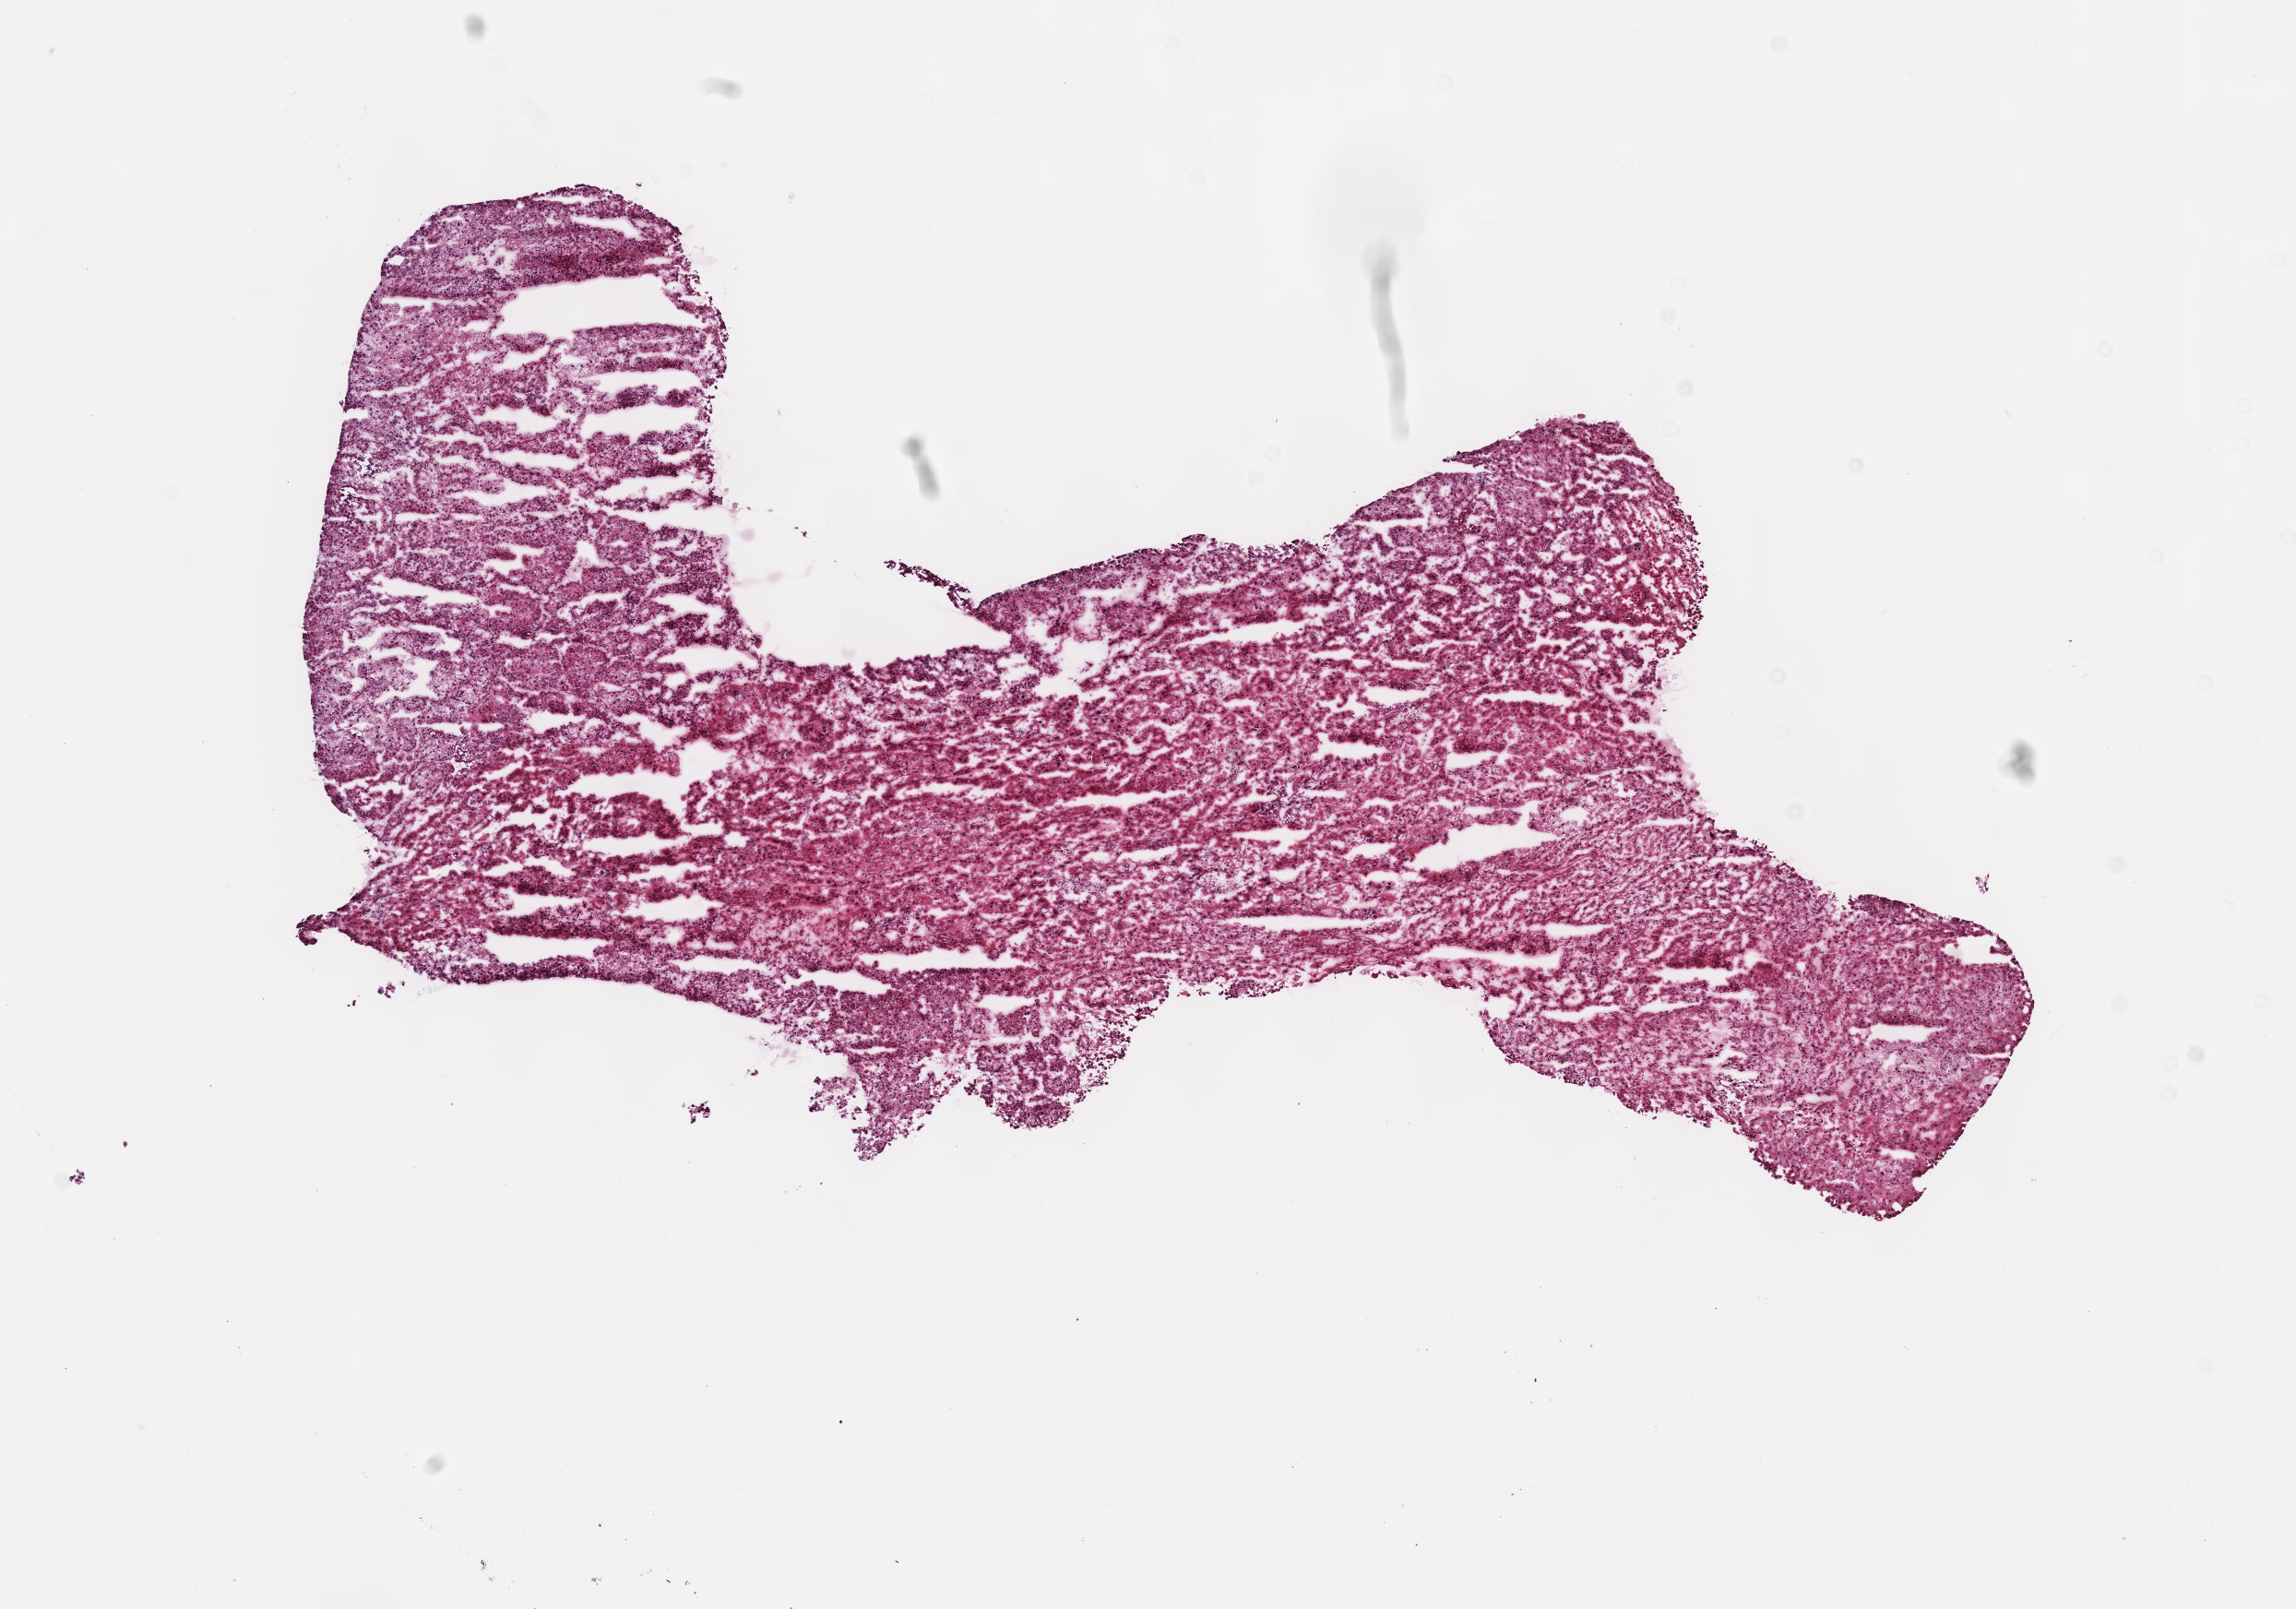
Digitized H&E tissue section (whole slide) — a low-resolution overview of the entire scanned area, about 10.1 x 7.1 mm (acquisition: 40x scan). Frozen section from the top of the tissue portion. Sample: primary tumour, liver. Male, age 58 years at initial diagnosis. Histologic grade: G4 (undifferentiated). Slide review estimates, as recorded: tumour cells 90%, tumour nuclei 95%, normal cells 0%, stromal cells 10%, necrosis 0%. Infiltration values recorded for this section: lymphocyte infiltration 0%, monocyte infiltration 0%, neutrophil infiltration 0%.
• pathologic diagnosis: Hepatocellular carcinoma, NOS
• AJCC pathologic stage: I